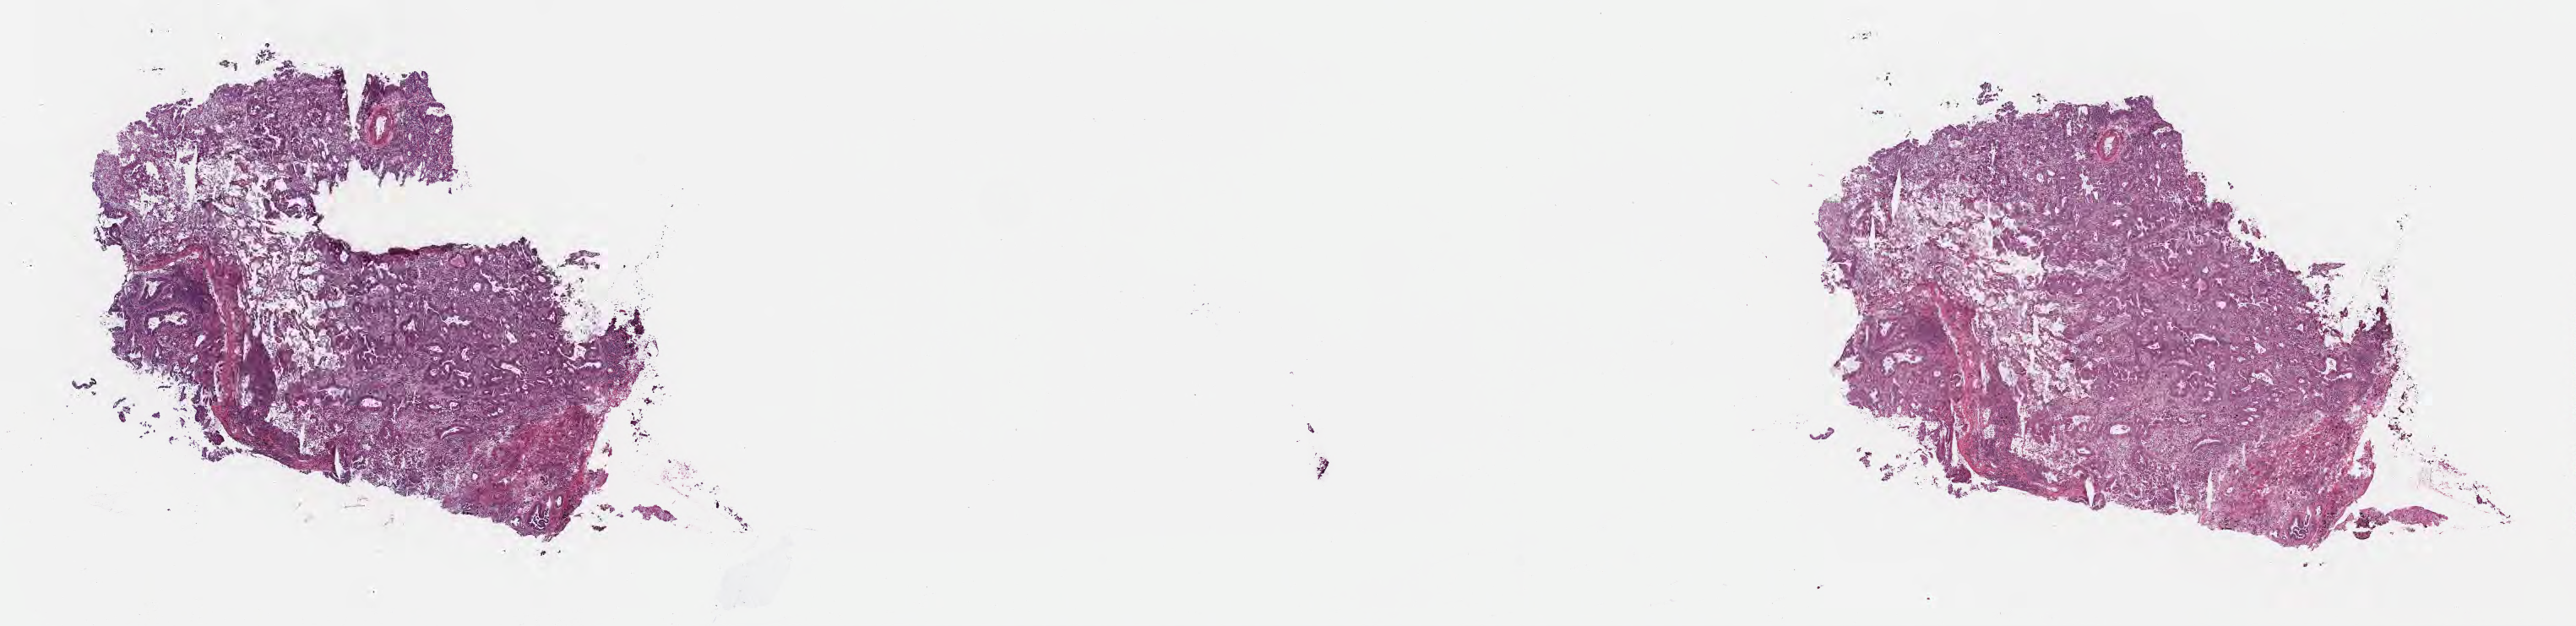
Haematoxylin and eosin whole-slide image, a low-resolution overview of the entire scanned area, about 24.7 x 6.0 mm, frozen section, primary tumor, anatomic site: middle lobe of right lung. Male patient, 79 years old. Pathologist review of this section (percent, as recorded): tumor cells 60%, tumor nuclei 60%, stromal cells 29%, necrosis 1%, normal cells 10%. Inflammatory infiltration, as recorded: lymphocyte infiltration 5%, monocyte infiltration 10%, neutrophil infiltration 4%.
AJCC pathologic stage: Stage IA. Histologic diagnosis: Adenocarcinoma, NOS. Section: top of the tissue portion.